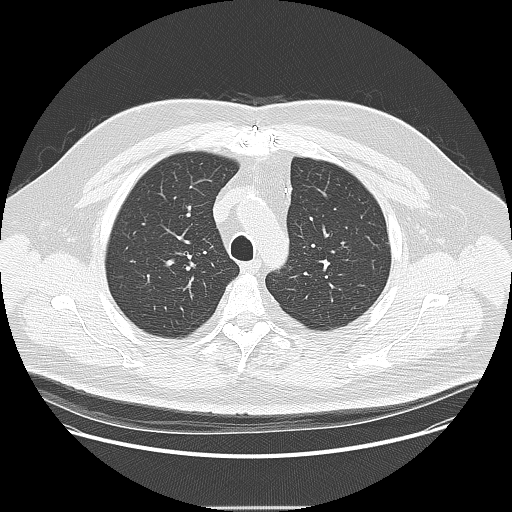
Low-dose screening chest CT, one axial slice. Position 115 of 157 along the scan axis. 120 kVp. Lung window (W 1500 / L -600 HU). 2.5 mm slice thickness. 512 × 512 image matrix, field of view 410 × 410 mm.
Annotated regions visible in this slice (expert manual segmentation):
- lesion 1 (tumor, upper lobe of left lung): bounding box (x1, y1, x2, y2) in pixels: (386, 241, 390, 245)